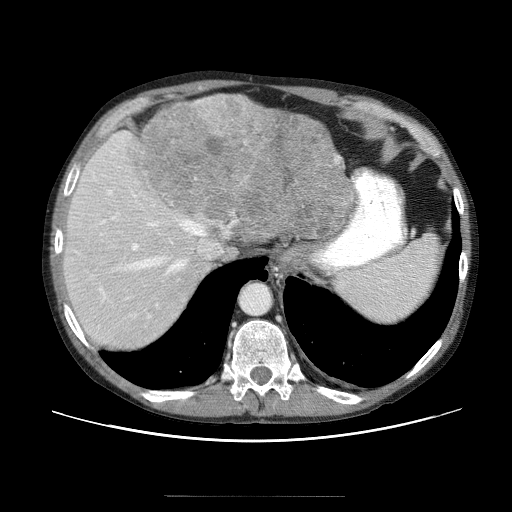
Contrast-enhanced abdominal CT (liver protocol), one axial slice. Position 47 of 69 along the scan axis. Reconstruction kernel STANDARD. 120 kVp. Soft-tissue window (W 400 / L 40 HU). 2.5 mm slice thickness. 512 × 512 image matrix. From the clinical record (not read from this slice): diagnosis: hepatocellular carcinoma (patient treated with transarterial chemoembolisation; whether this scan precedes or follows treatment is not stated here); TNM stage (as recorded): Stage-IVB; Child-Pugh class: B; tumour differentiation: poorly differentiated; tumour nodularity: multinodular.
Annotated regions visible in this slice (semi-automatic segmentation, software-assisted and operator-edited):
- liver parenchyma outside the tumour (the mass and vessels are separate outlines, so this box may not span the whole liver): bounding box <62,94,245,354> (left, top, right, bottom; pixels)
- mass: <140,94,358,255>
- liver vessels: <100,141,166,321>